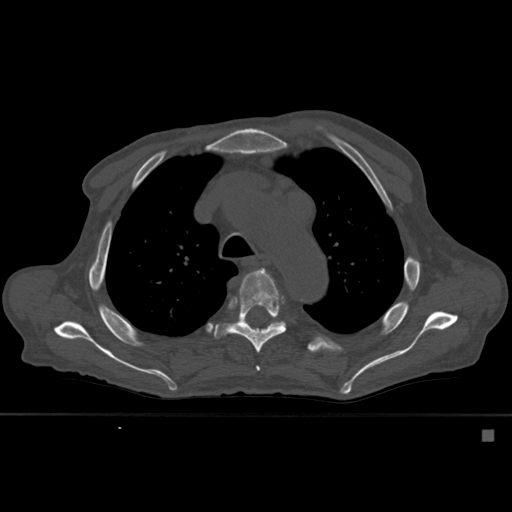
CT including the spine, one axial slice. Position 402 of 527 along the scan axis. Bone window (W 1800 / L 400 HU). 512 × 512 image matrix, field of view 373 × 373 mm. Male patient, age 78 years. From the clinical record (not read from this slice): primary cancer: prostate.
Annotated regions visible in this slice (semi-automatically segmented with operator editing):
- T4 vertebra: bounding box [x1, y1, x2, y2] px = [256, 269, 264, 371]
- T5 vertebra: [214, 269, 287, 353]